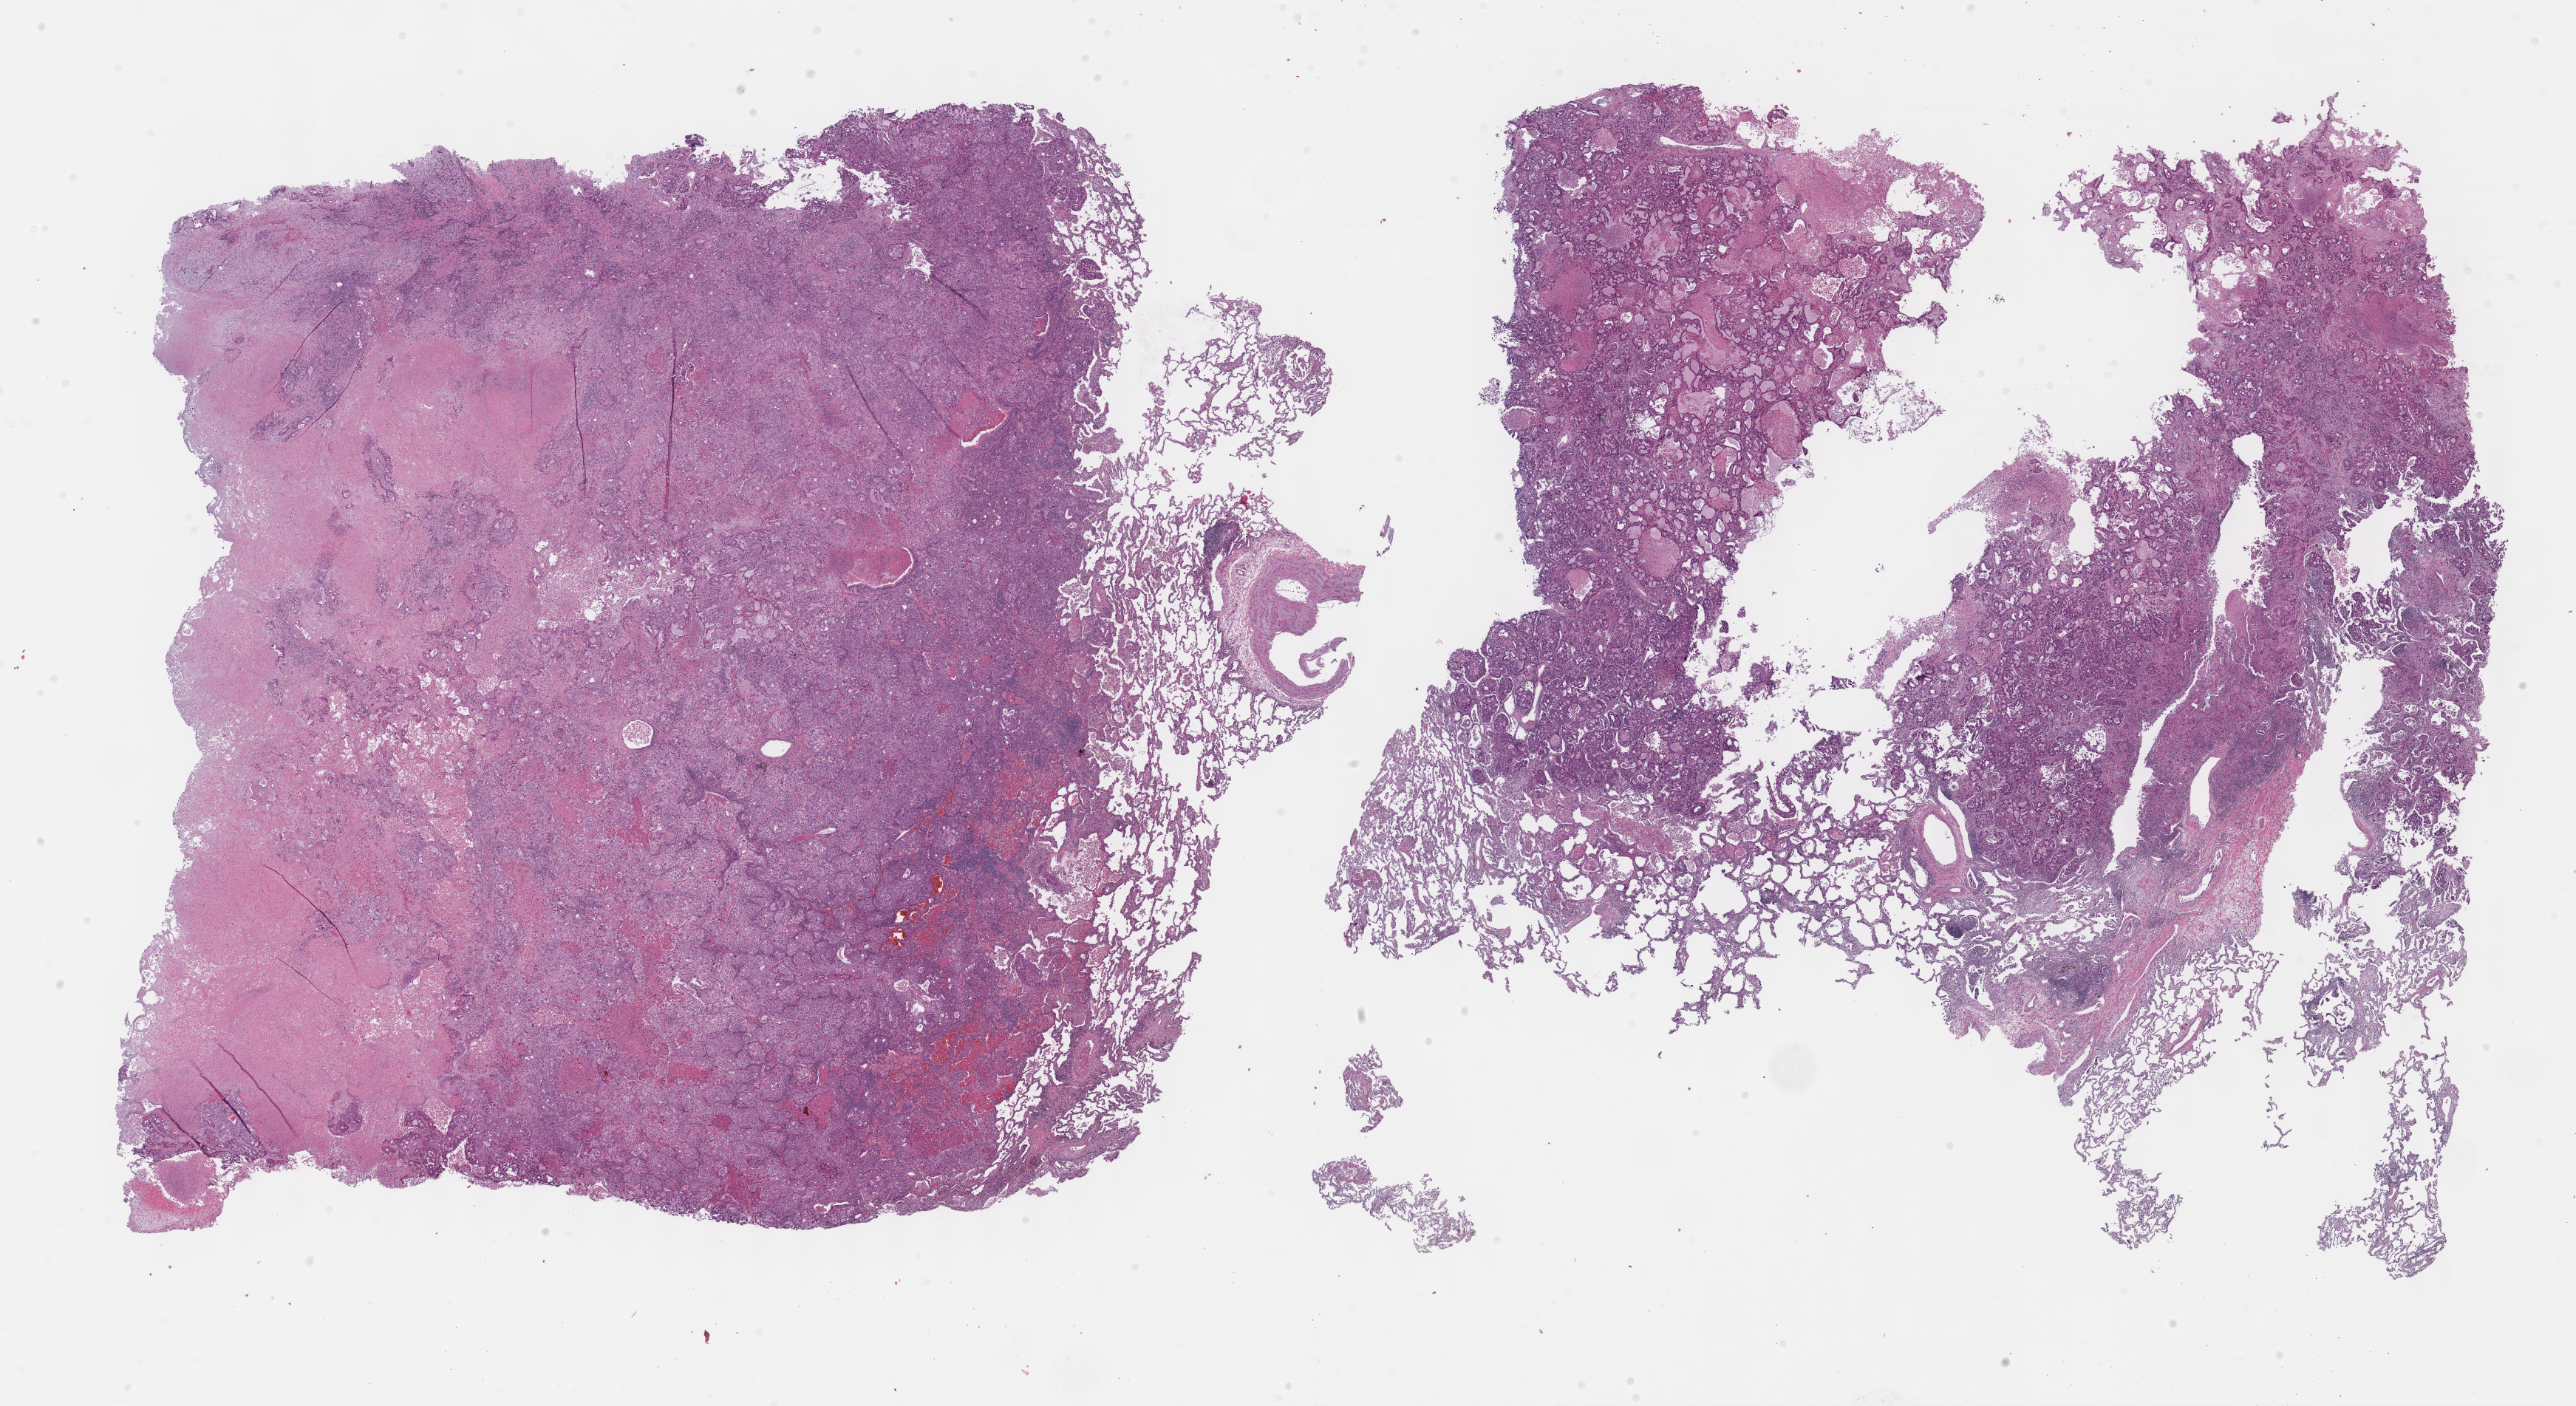
Whole-slide histology image, H&E, shown as a low-resolution overview of the whole scanned area (about 28.2 x 15.4 mm, acquisition: 40x scan), formalin-fixed paraffin-embedded (FFPE) diagnostic section, lung, primary tumour sample. Female, age 58 years at initial diagnosis.
Laterality: right. AJCC pathologic stage: IIA. Pathologic diagnosis: Adenocarcinoma, NOS (upper lobe, lung).